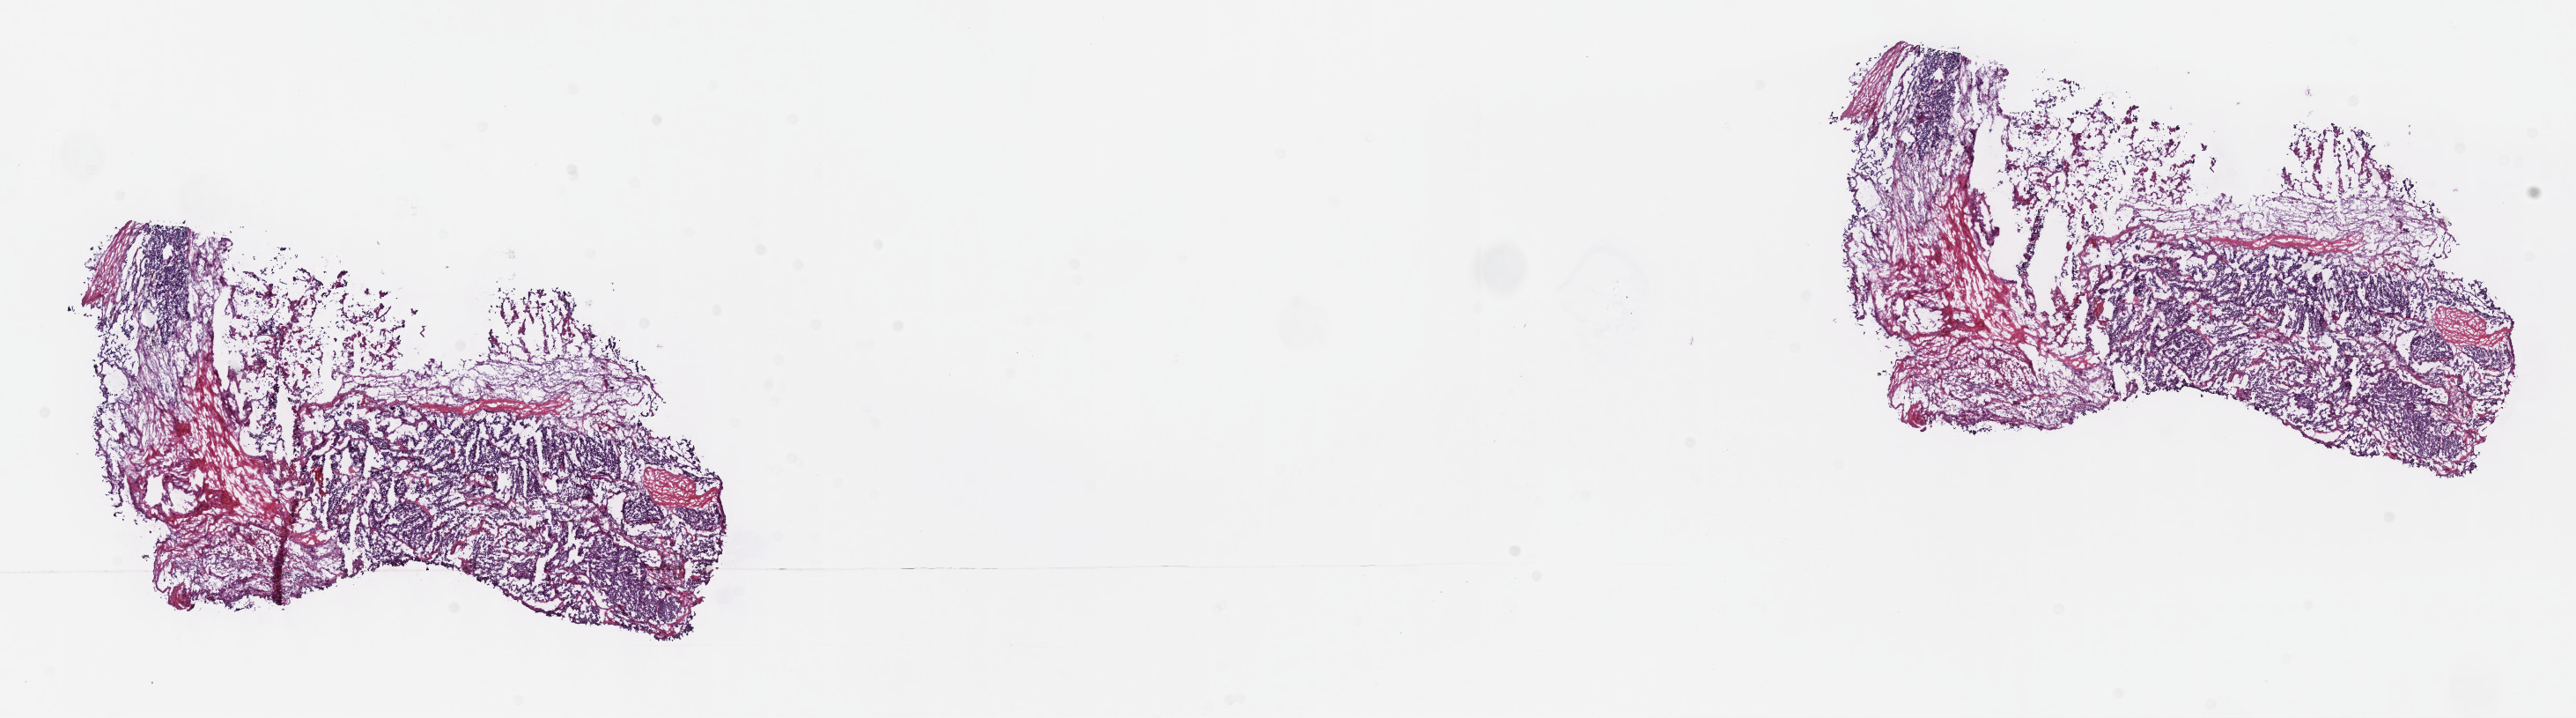
H&E whole-slide image, whole scanned area (about 23.7 x 6.6 mm, from a 40x scan) shown as a low-resolution overview. FFPE section. Breast, primary tumour sample. Patient: female, age at initial diagnosis 35 years.
AJCC pathologic stage: IV (7th edition). Histologic diagnosis: Infiltrating duct carcinoma, NOS.